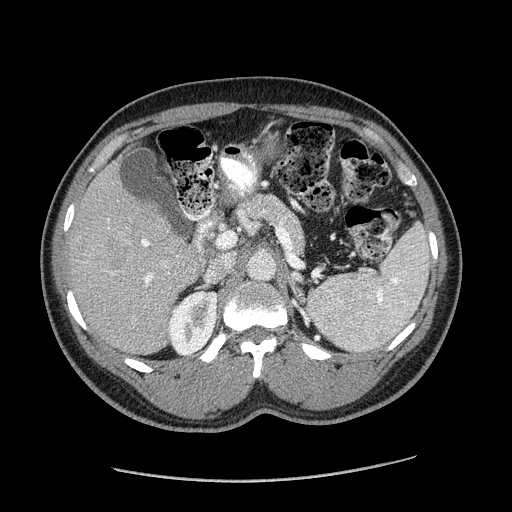
Contrast-enhanced abdominal CT (liver protocol), one axial slice; slice 101 of 182 in the series (ordered by position); reconstruction kernel STANDARD; 120 kVp; soft-tissue window (W 400 / L 40 HU); 2.5 mm slice thickness; 512 × 512 image matrix. From the clinical record (not read from this slice): diagnosis: hepatocellular carcinoma (patient treated with transarterial chemoembolisation; whether this scan precedes or follows treatment is not stated here); TNM stage (as recorded): Stage-I; Child-Pugh class: A; tumour differentiation: well differentiated; tumour nodularity: uninodular.
Annotated regions visible in this slice (semi-automatic segmentation, software-assisted and operator-edited):
- liver parenchyma outside the tumour (the mass and vessels are separate outlines, so this box may not span the whole liver): box from (x=68, y=156) to (x=206, y=354) px
- mass: (x=97, y=231)–(x=135, y=278)
- liver vessels: (x=141, y=239)–(x=153, y=284)